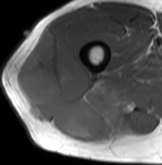
MRI of an extremity soft-tissue mass, one axial slice; slice 50 of 61 in the series (ordered by position); MR volume resampled by the dataset authors to the PET/CT grid (not the native acquisition matrix); 3.27 mm slice thickness; 162 × 165 image matrix, field of view 158 × 161 mm. Male patient. Case-level facts recorded for this patient, not image findings: histological type: poorly differentiated synovial sarcoma; grade: high; site of the primary tumour: right buttock.
Annotated regions visible in this slice (expert contour drawn on MRI and transferred to this co-registered scan by the dataset authors):
- gross tumour volume including surrounding oedema: bounding box [x1, y1, x2, y2] px = [16, 29, 120, 142]
- gross tumour volume (mass): [16, 29, 120, 142]